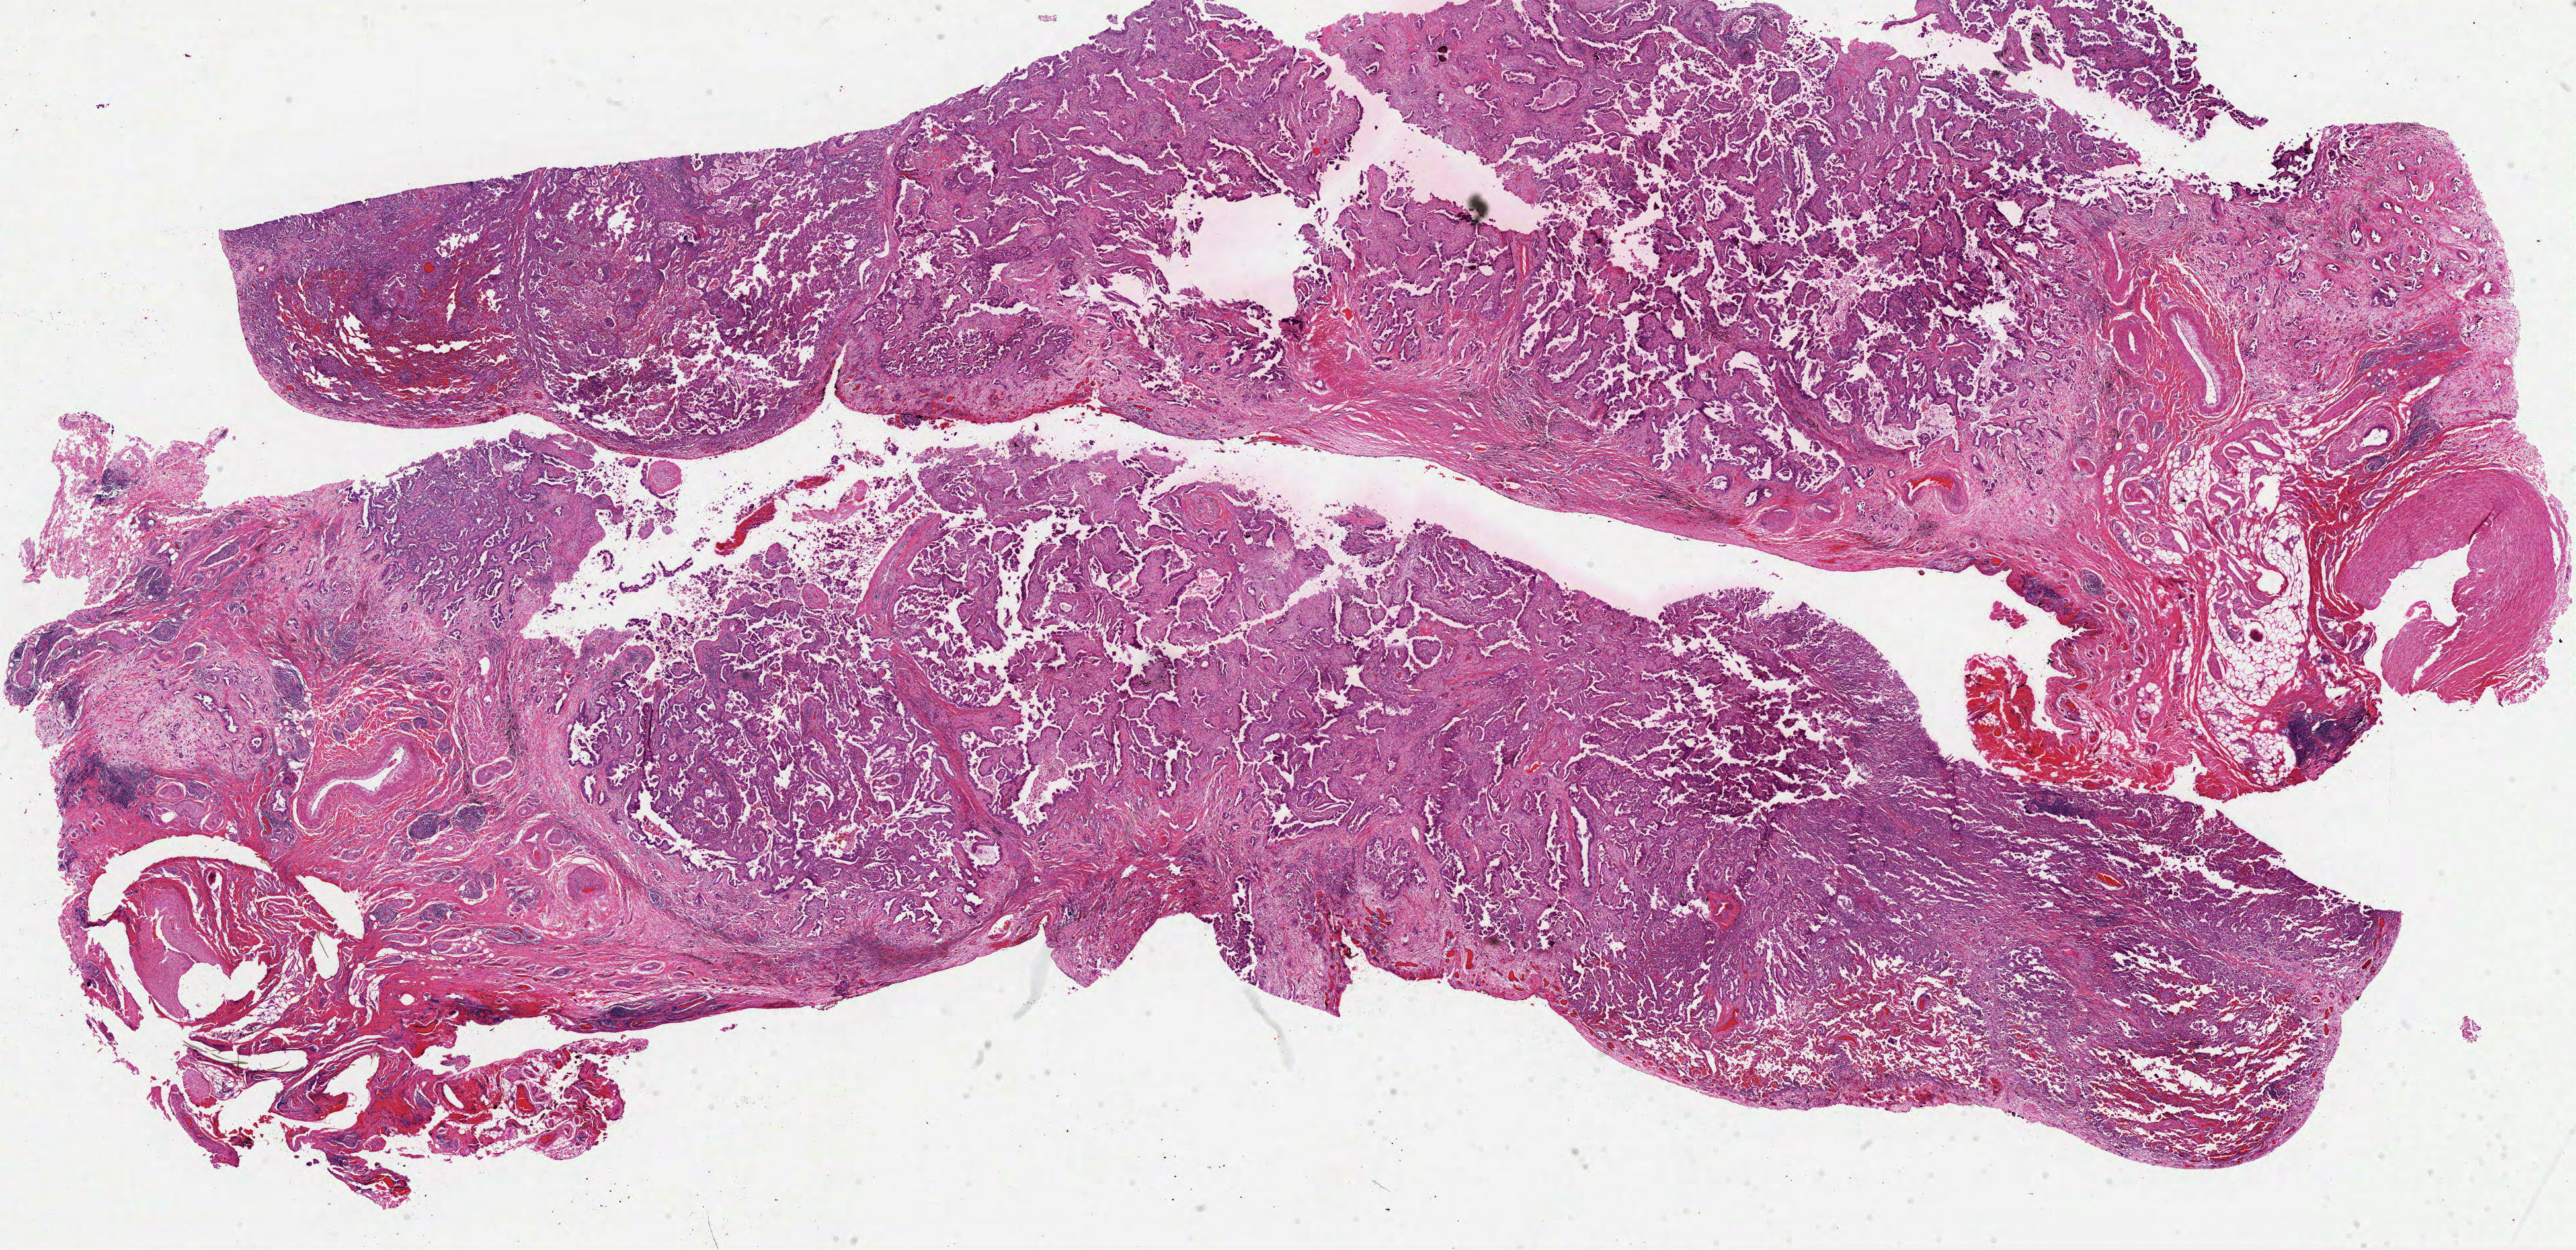
Digitized H&E tissue section (whole slide) — low-resolution overview of the scanned area, about 31.4 x 15.3 mm (slide scanned at 40x). Formalin-fixed paraffin-embedded (FFPE) diagnostic section. Sample: primary tumour, lung. Female patient; age at initial diagnosis 45 years.
AJCC pathologic stage: IIIA (4th edition). Laterality: left. Diagnosis: Adenocarcinoma, NOS (upper lobe, lung).